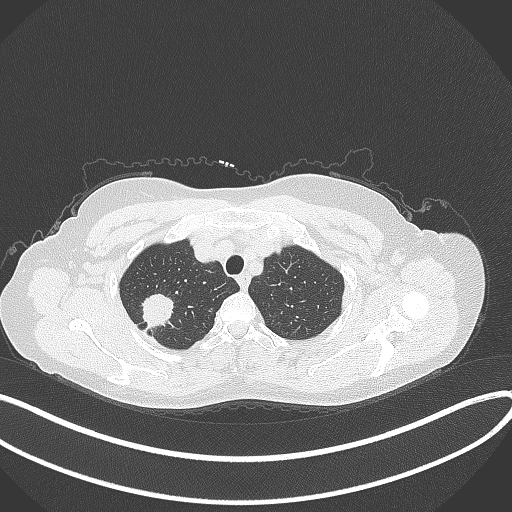
Chest CT, one axial slice. Slice 311 of 337 in the series (ordered by position). 120 kVp. Lung window (W 1500 / L -600 HU). 1 mm slice thickness. 512 × 512 image matrix. Female patient, age 50 years. Case-level facts recorded for this patient, not image findings: clinical TNM (as recorded): T1c N0 M0; histopathological grade: G2-3.
Outlined on this slice (bounding box drawn by a radiologist):
- lung tumour (recorded histology: adenocarcinoma): box from (x=136, y=291) to (x=177, y=331) px